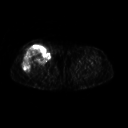
FDG PET of an extremity soft-tissue mass (from a PET/CT study), one axial slice; slice 247 of 311 in the series (ordered by position); 3.27 mm slice thickness; 128 × 128 image matrix. Patient: female, 57 years. Case-level facts recorded for this patient, not image findings: histological type: pleiomorphic undifferentiated sarcoma; grade: high; site of the primary tumour: right quadricep.
Structures marked on this image (expert contour drawn on MRI and transferred to this co-registered scan by the dataset authors):
- tumour plus oedema (research contour): box from (x=23, y=46) to (x=49, y=72) px
- tumour (research contour): (x=23, y=46)–(x=49, y=72)